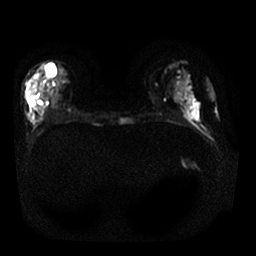
Breast MRI, one axial slice; position 11 of 30 along the scan axis; diffusion-weighted series; image 2 of 4 stored at this slice position (different b-values; order by instance number); 1.5 T; 4 mm slice thickness; 256 × 256 image matrix. Female patient.
Annotated regions visible in this slice (manually delineated by an expert):
- tumour on diffusion-weighted imaging: bounding box <26,83,46,129> (left, top, right, bottom; pixels)